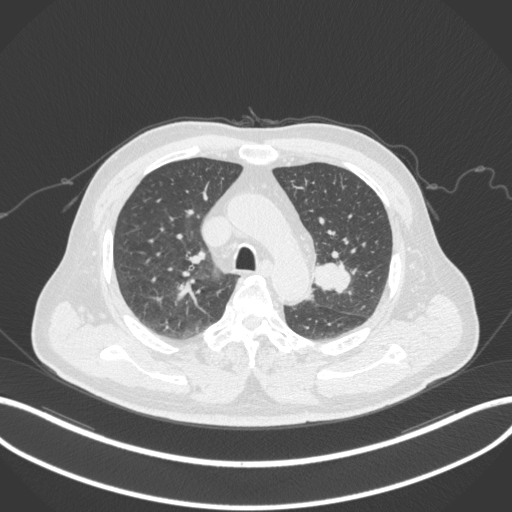
Chest CT, one axial slice. Position 212 of 286 along the scan axis. Reconstruction kernel B31f. 120 kVp. Lung window (W 1500 / L -600 HU). 1 mm slice thickness. 512 × 512 image matrix, field of view 400 × 400 mm. Patient: male, 67 years. From the clinical record (not read from this slice): clinical TNM (as recorded): T2a N1 M0; histopathological grade: G3.
Structures marked on this image (rectangle marked by the reading radiologist):
- lung tumour (recorded histology: adenocarcinoma): bounding box [x1, y1, x2, y2] px = [311, 259, 353, 296]